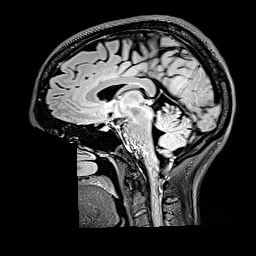
Brain MRI from a brain-tumour surgery series, one sagittal slice; position 85 of 176 along the scan axis; T2 FLAIR; 1 mm slice thickness; 256 × 256 image matrix, field of view 256 × 256 mm. Case-level facts recorded for this patient, not image findings: histopathology: Oligodendroglioma; WHO grade: 2; IDH mutation: yes; tumour location: Right Parietal.
Annotated regions visible in this slice (outlined manually by an expert reader):
- tumour: bounding box [x1, y1, x2, y2] px = [170, 74, 188, 95]